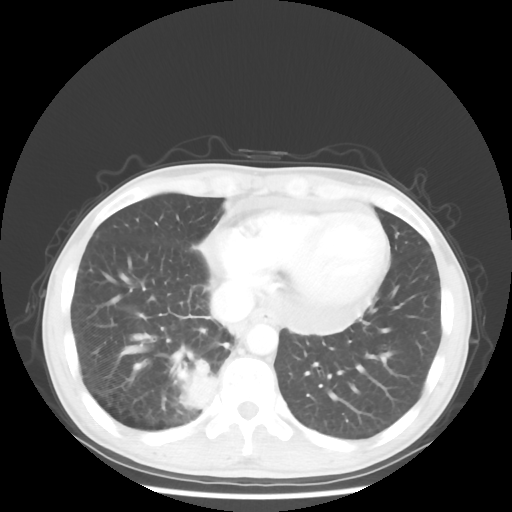
Chest CT, one axial slice. Slice 14 of 58 in the series (ordered by position). Reconstruction kernel STANDARD. Lung window (W 1500 / L -600 HU). 5 mm slice thickness. 512 × 512 image matrix, field of view 360 × 360 mm. Male patient, age 56 years. From the clinical record (not read from this slice): clinical TNM (as recorded): T2 N1 M1; histopathological grade: G1.
Outlined on this slice (bounding box drawn by a radiologist):
- lung tumour (recorded histology: adenocarcinoma): bounding box [x1, y1, x2, y2] px = [178, 359, 220, 418]